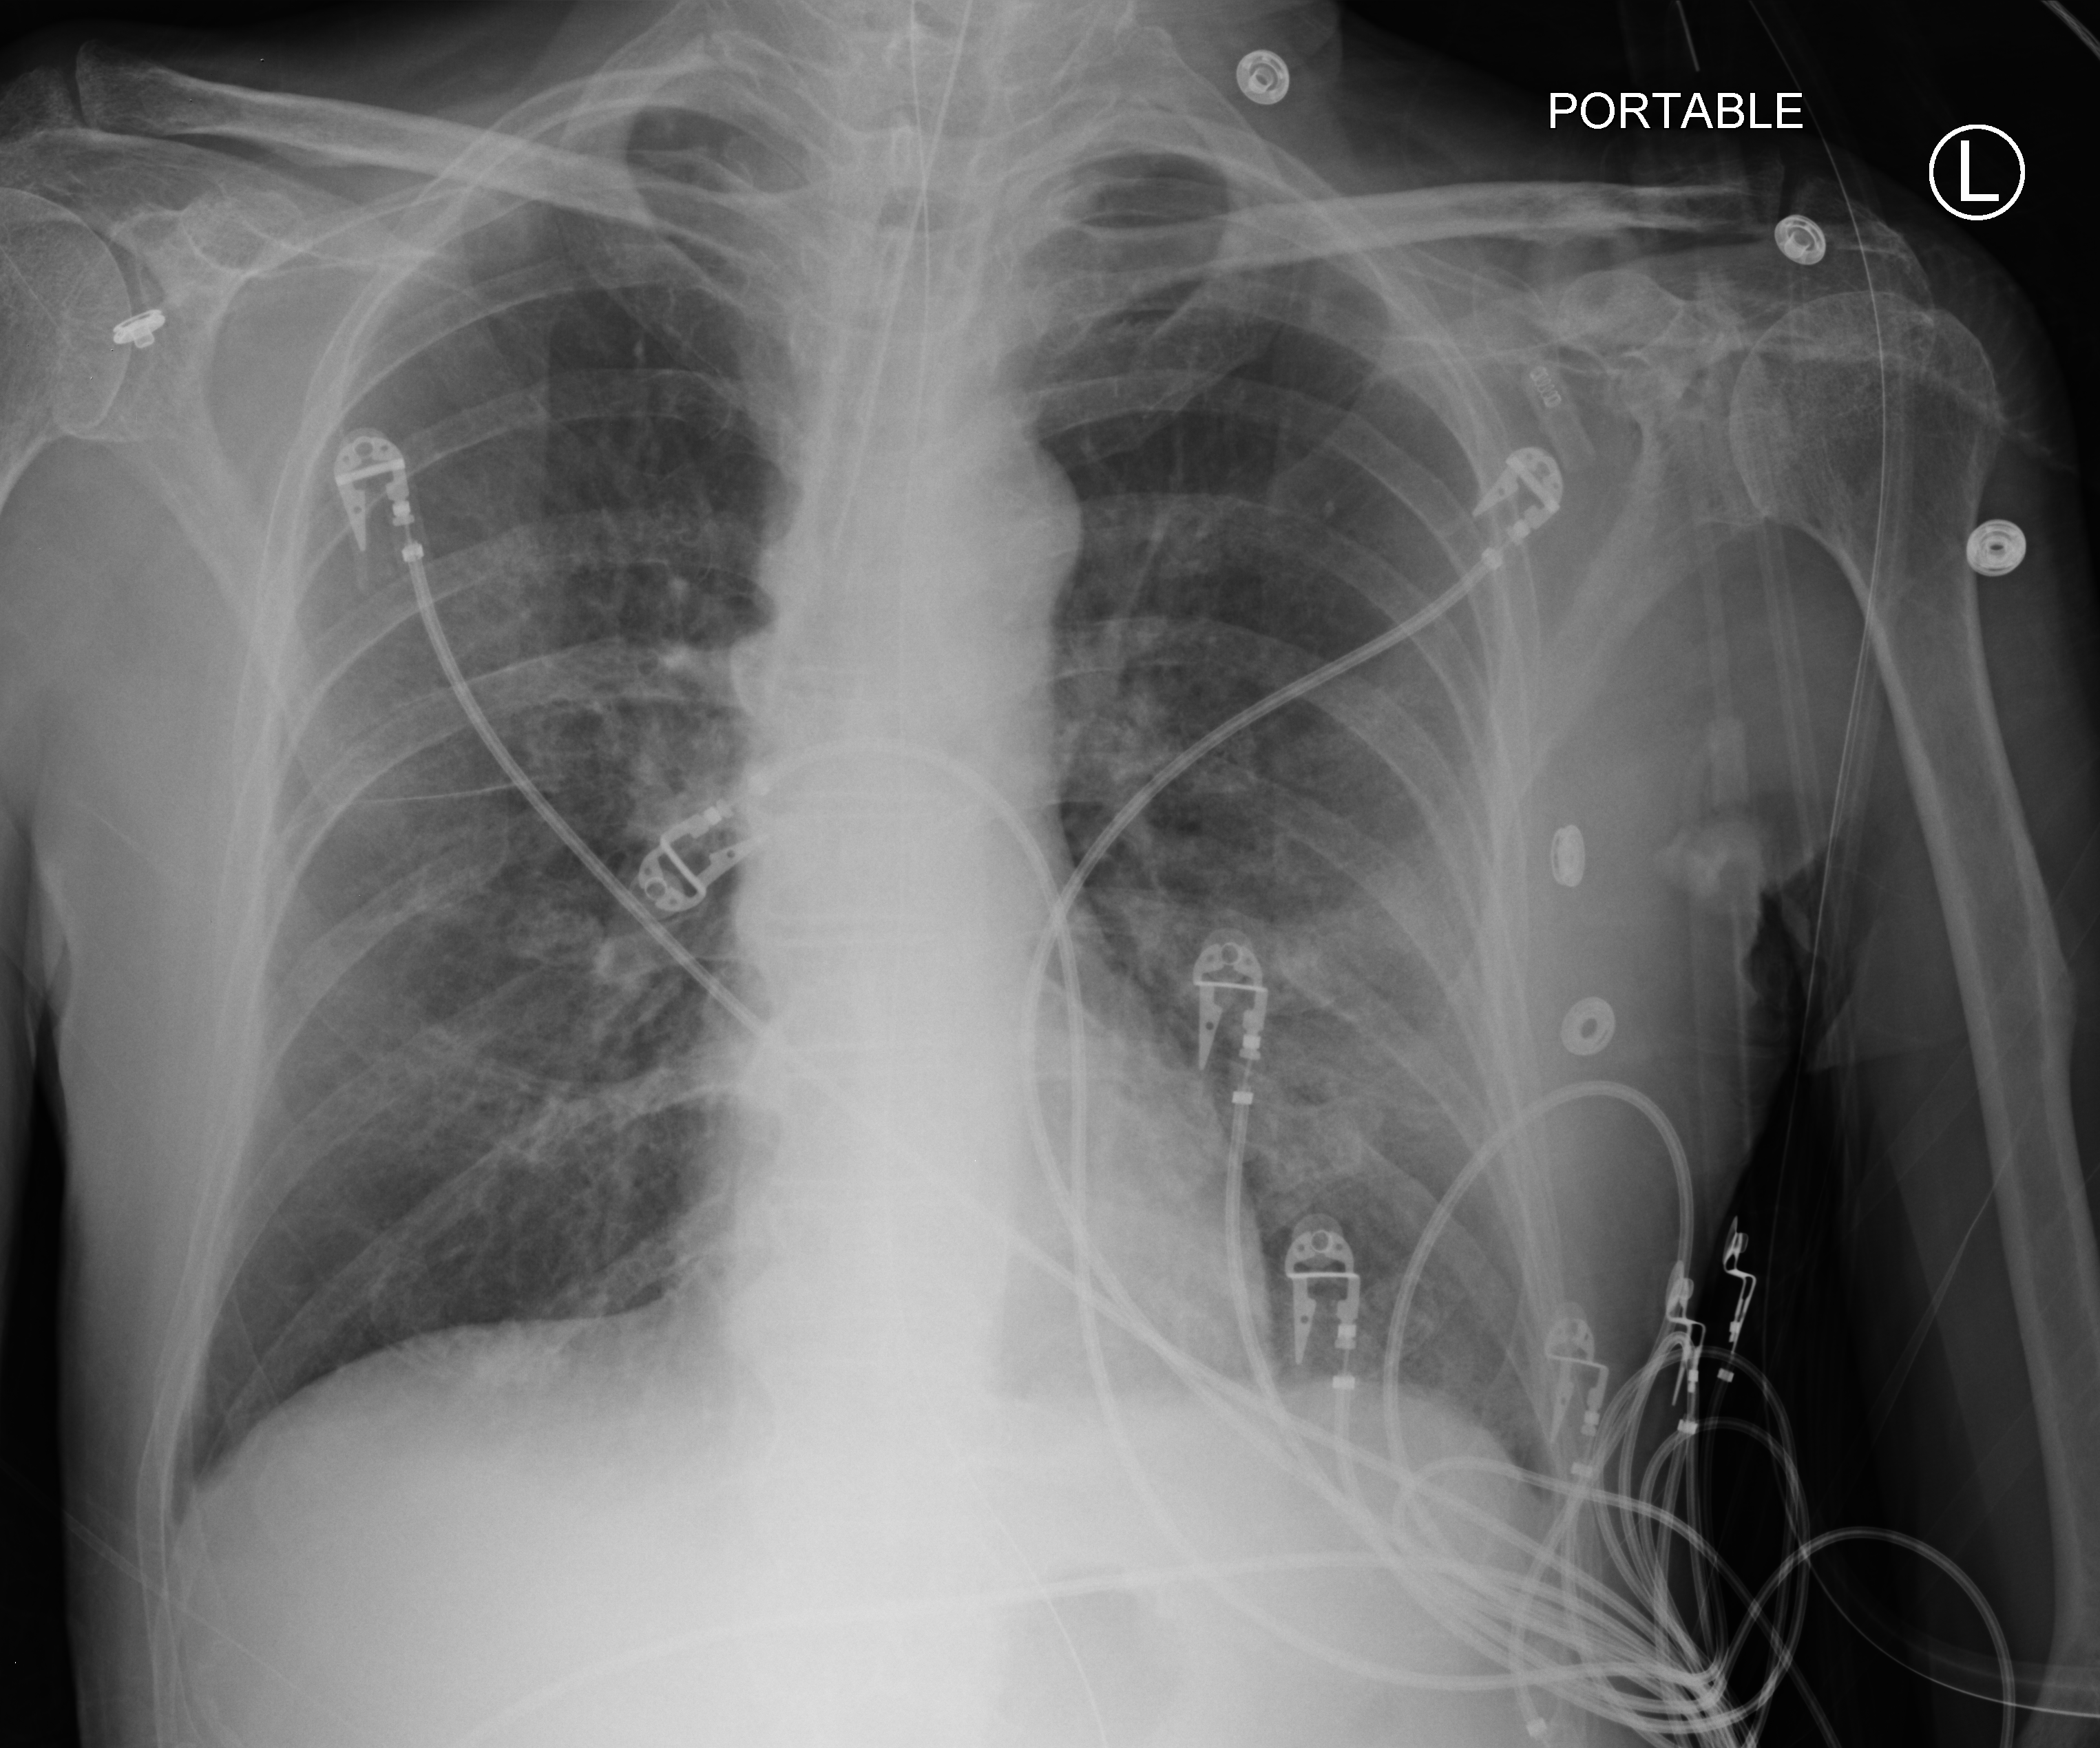
Bedside chest radiograph (computed radiography), anteroposterior (AP) projection. Patient hospitalised with COVID-19; male, aged 60–74 years.
Admission-level facts for this patient (not findings on this image; timing relative to this image not recorded): hypertension (admission record): yes; diabetes (admission record): yes; admitted to intensive care during this hospital stay: yes.